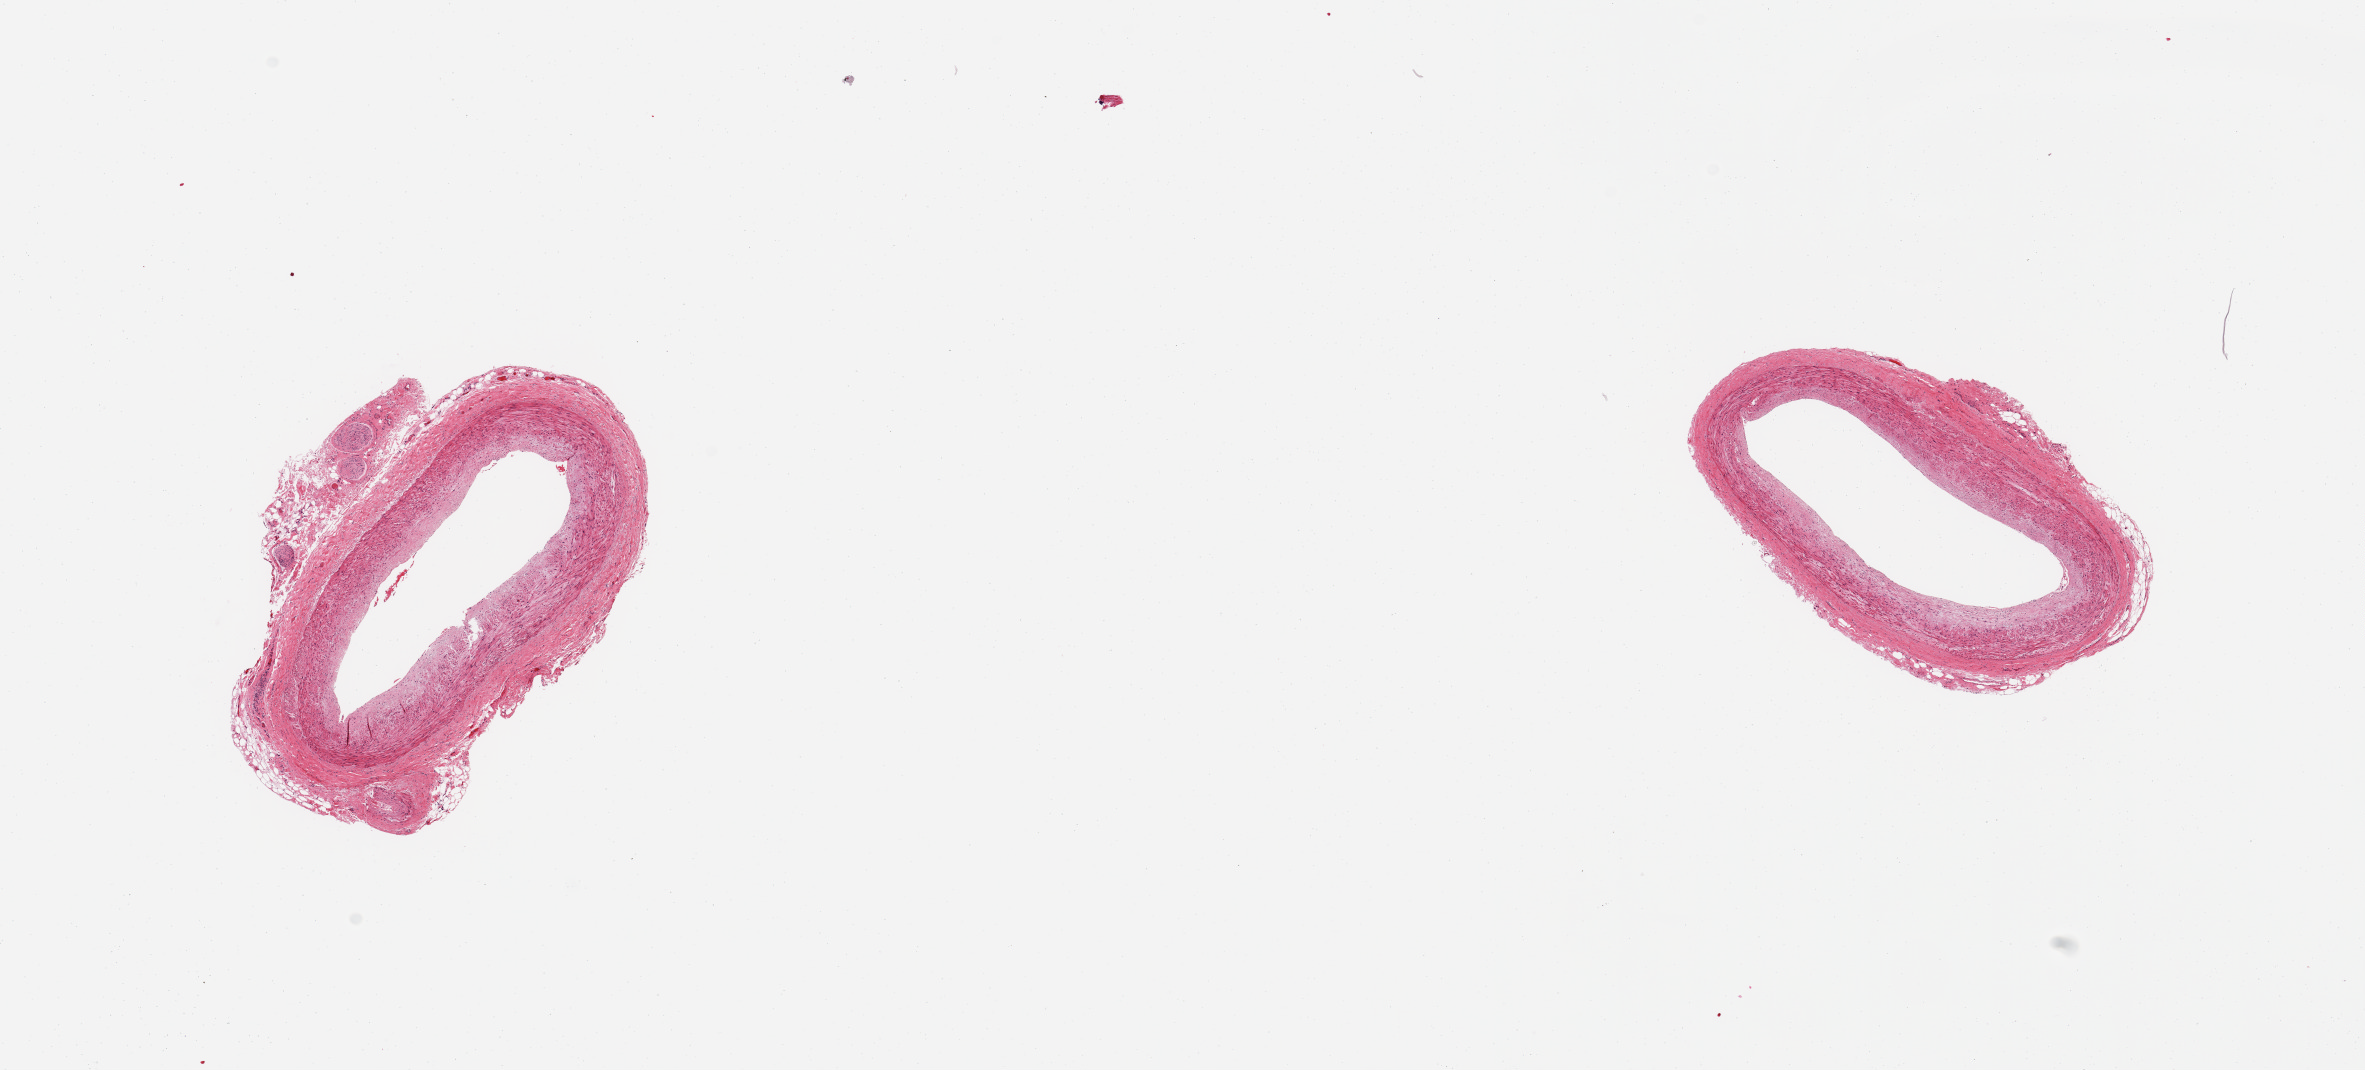
Whole-slide image, H&E stain, brightfield, whole scanned area (about 18.7 x 8.5 mm, from a 20x scan) shown as a low-resolution overview. PAXgene-fixed, paraffin-embedded tissue. Sampled site (target tissue): coronary artery. Donor tissue sample. Donor sex: male.
Pathologist's review note for this sample: 2 pieces, minimal atherosis; trace ~0.5mm nubbins fibrous tissue/peripheral nerve elements.